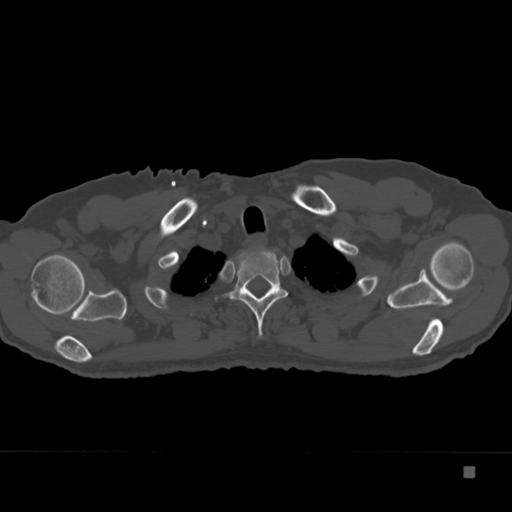
CT including the spine, one axial slice. Position 302 of 332 along the scan axis. Reconstruction kernel Br40s. Bone window (W 1800 / L 400 HU). 512 × 512 image matrix, field of view 389 × 389 mm. Patient: male, 72 years. From the clinical record (not read from this slice): primary cancer: skeletal.
Annotated regions visible in this slice (semi-automatically segmented with operator editing):
- T2 vertebra: bounding box <214,248,288,339> (left, top, right, bottom; pixels)
- T3 vertebra: <246,283,273,294>